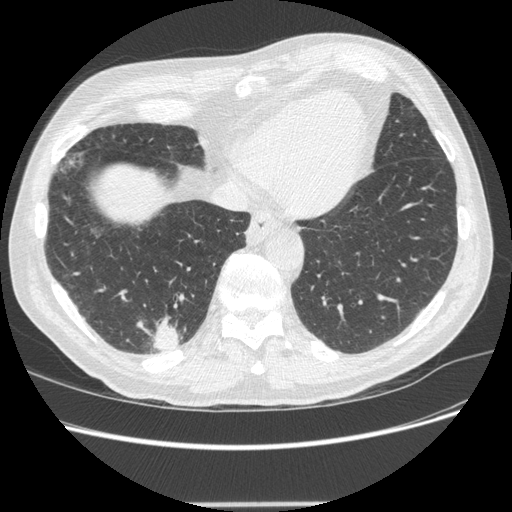
Low-dose screening chest CT, one axial slice. Position 62 of 245 along the scan axis. Reconstruction kernel STANDARD. 120 kVp. Lung window (W 1500 / L -600 HU). 512 × 512 image matrix, field of view 372 × 372 mm.
Annotated regions visible in this slice (manually delineated by an expert):
- lesion 1 (tumor, lower lobe of right lung): bounding box (x1, y1, x2, y2) in pixels: (152, 320, 181, 352)